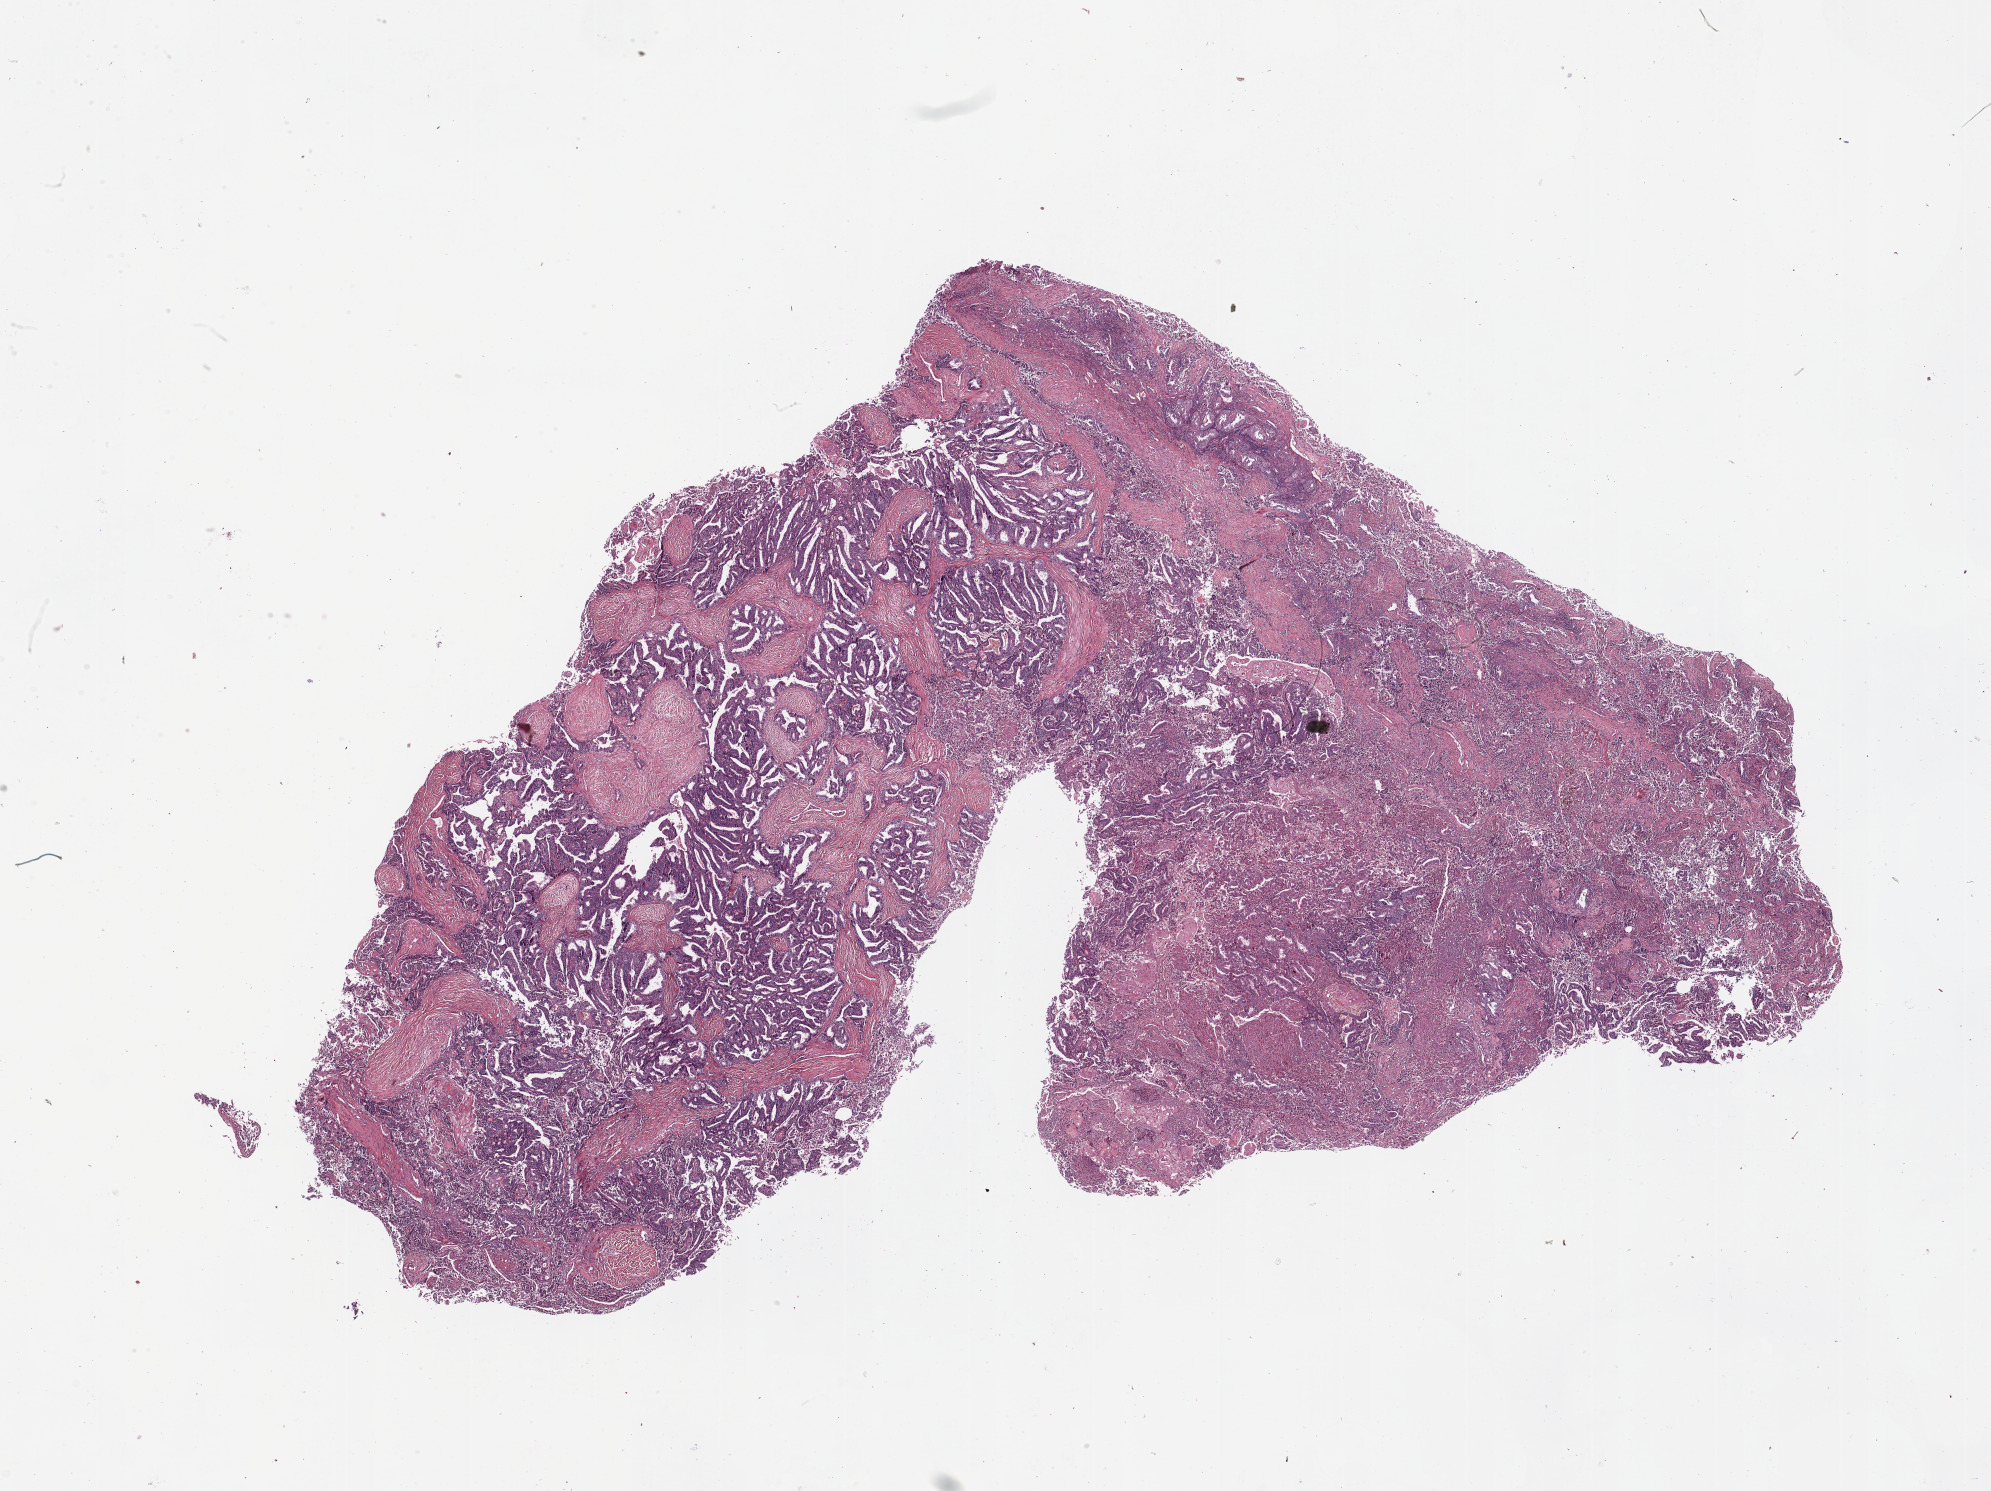
Whole-slide histology image, H&E — a low-resolution overview of the entire scanned area, about 15.8 x 11.8 mm (from a 20x scan); tumour tissue sample, uterus. 57-year-old female patient. Histologic grade: G2 (moderately differentiated).
AJCC pathologic stage: III. Diagnosis: Endometrioid adenocarcinoma, NOS.